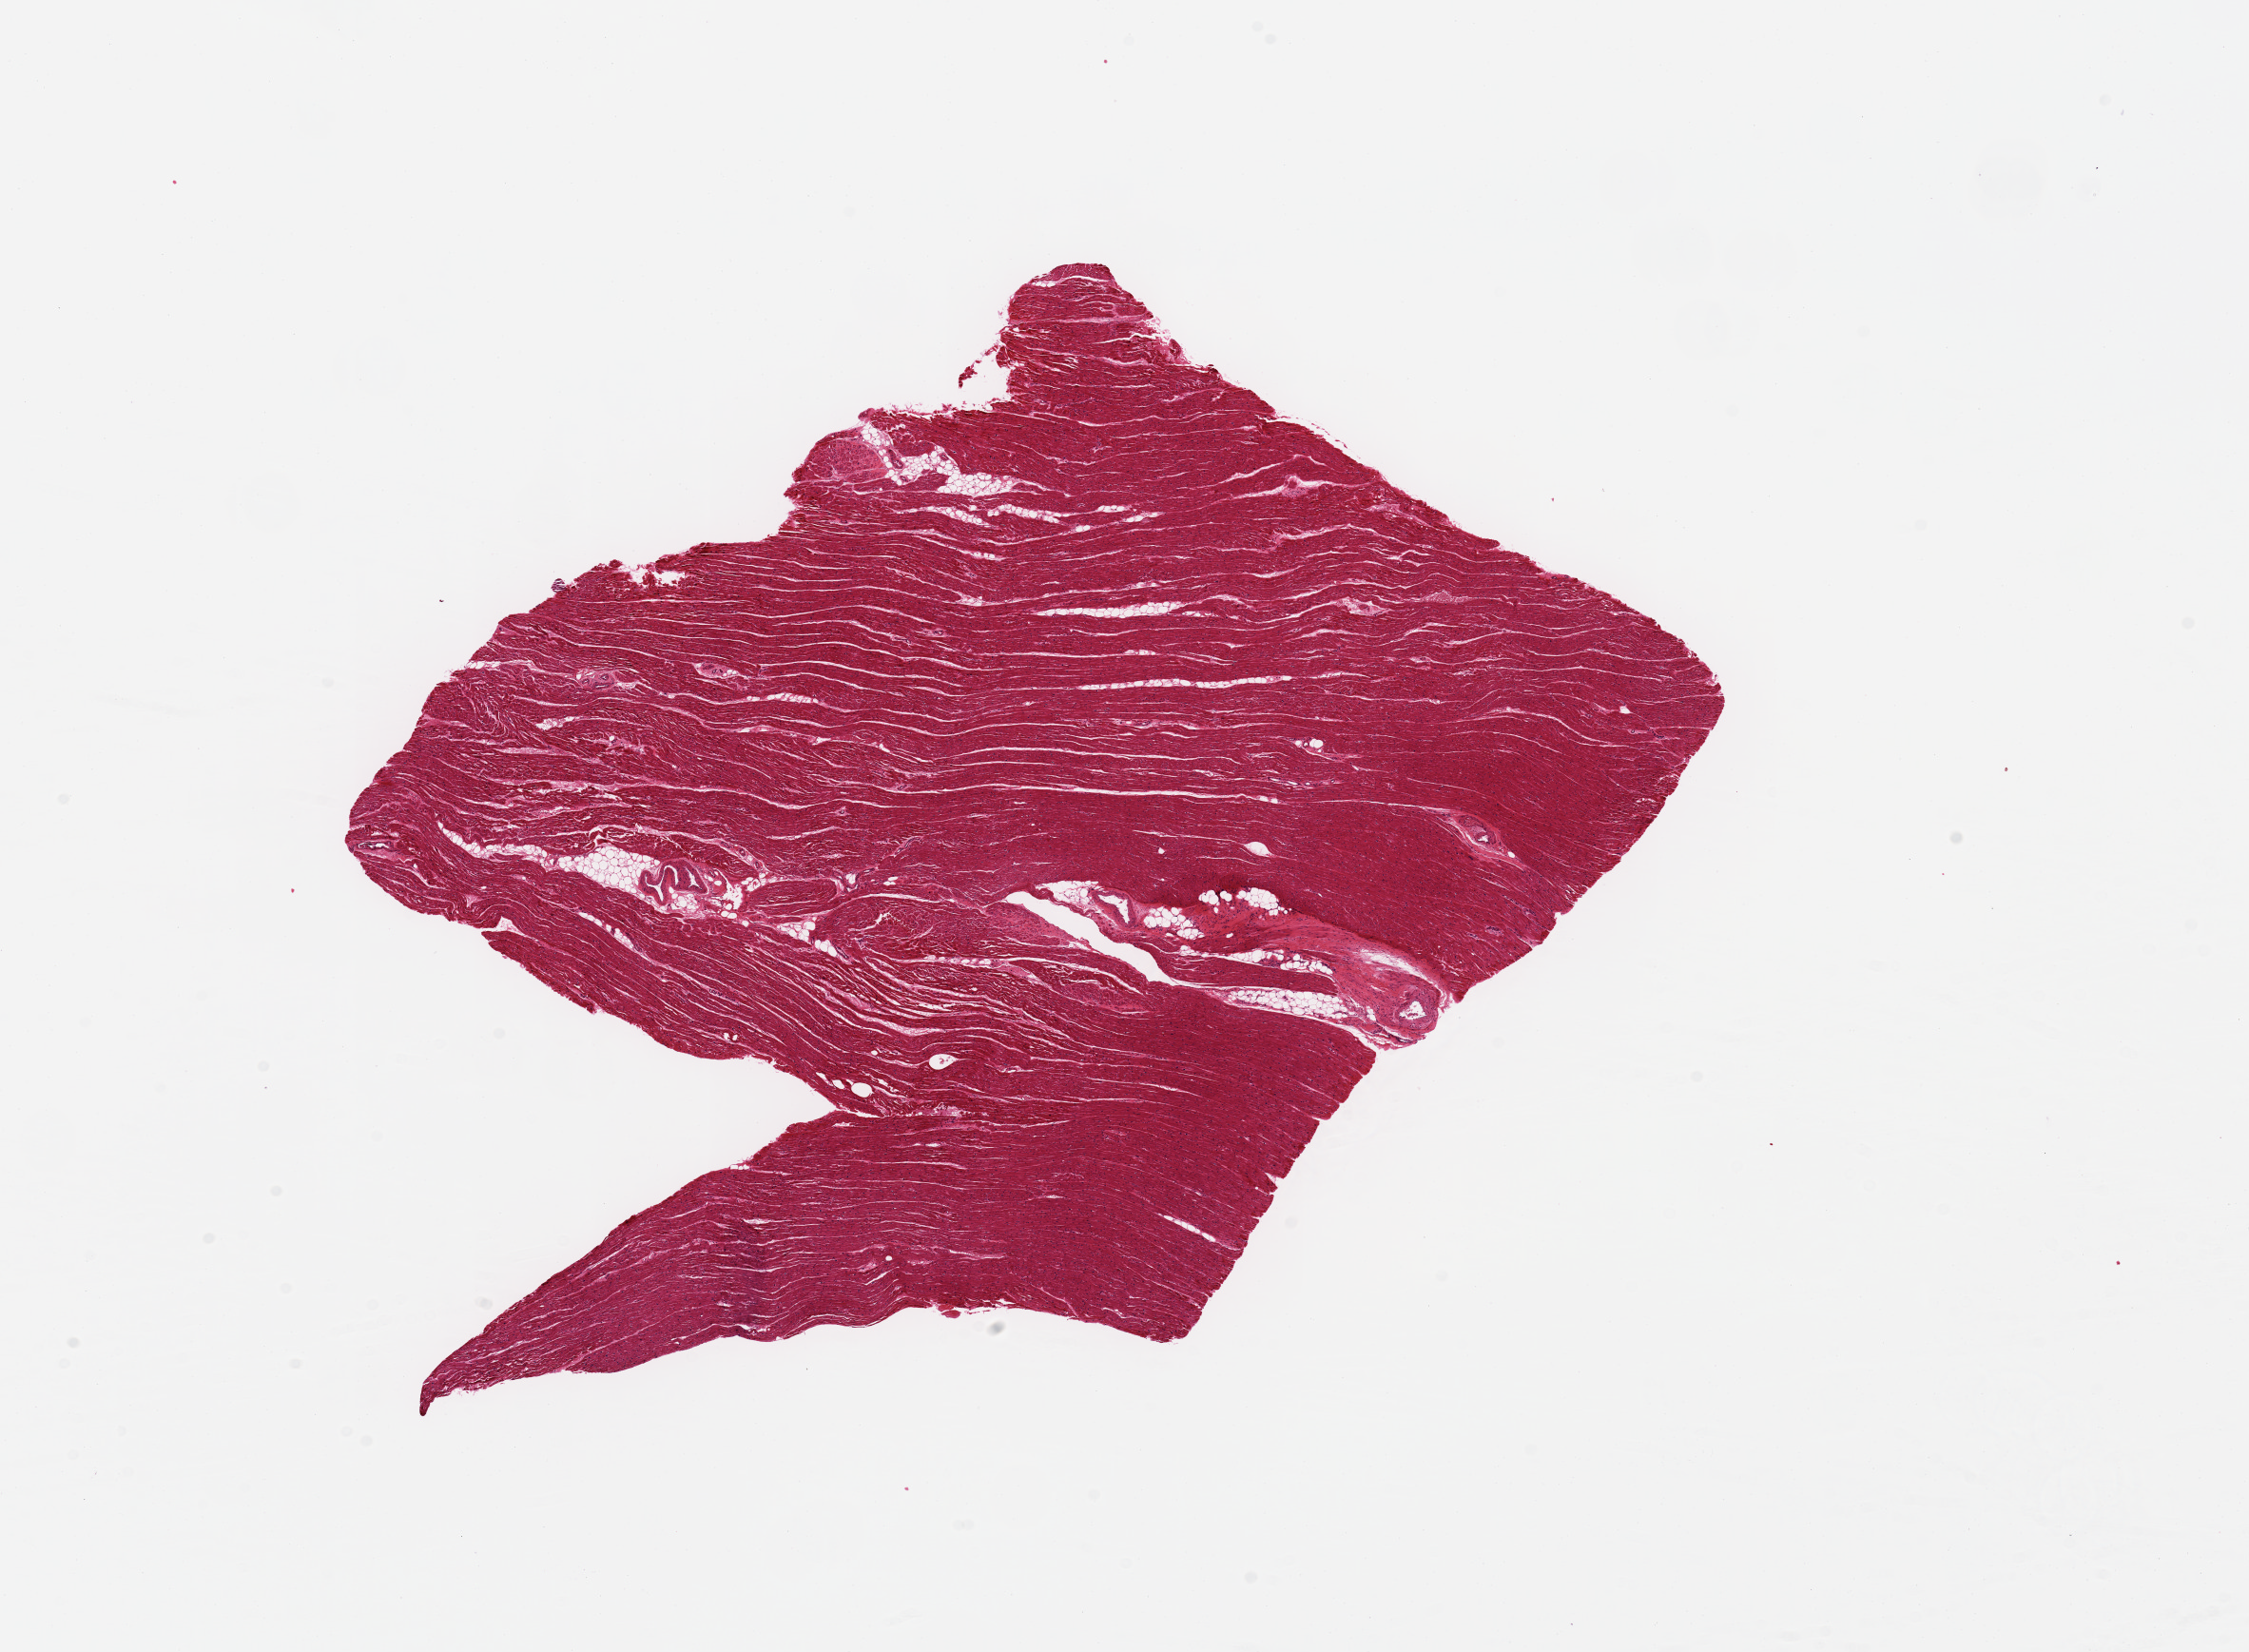
H&E whole-slide image, whole scanned area (about 18.7 x 13.7 mm, from a 20x scan) shown as a low-resolution overview, PAXgene-fixed paraffin-embedded (PFPE) section, section of heart (target tissue), tissue donor sample. Donor sex: male.
- pathologist's review note for this sample: Well preserved myocardium